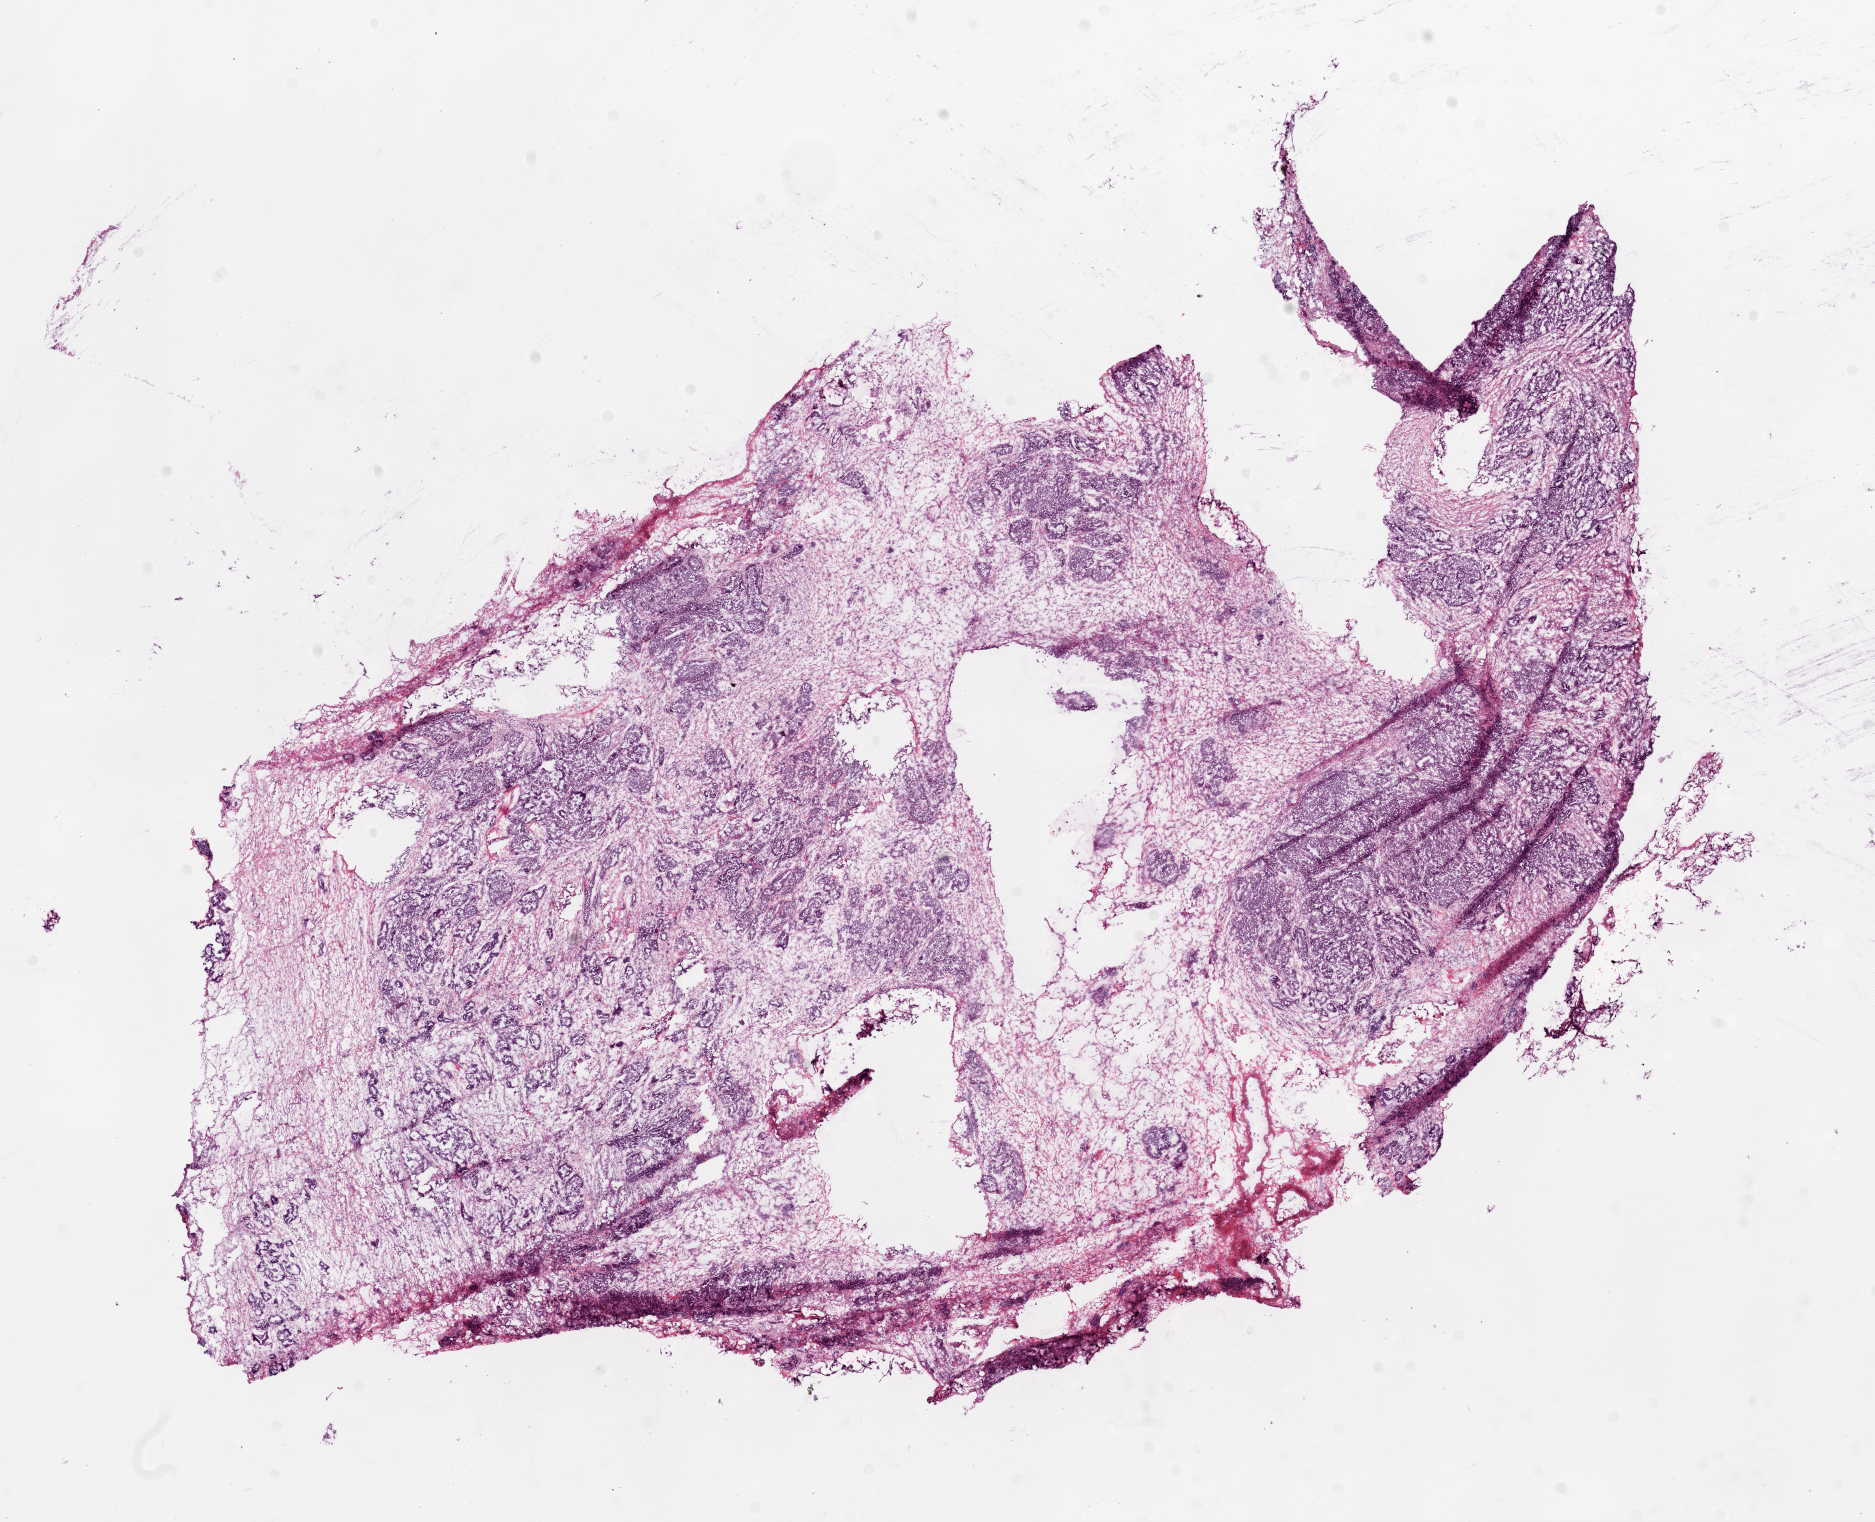
Hematoxylin and eosin (H&E) stained whole-slide image — low-resolution overview of the scanned area, about 15.0 x 12.2 mm, frozen section, sample: primary tumour, ovary. Female patient; age at initial diagnosis 47 years. Histologic grade: G3 (poorly differentiated). Composition of this section per pathologist review: tumour cells 55%, tumour nuclei 74%, normal cells 43%, stromal cells 0%, necrosis 2%.
Histologic diagnosis: Serous cystadenocarcinoma, NOS (specified parts of peritoneum).